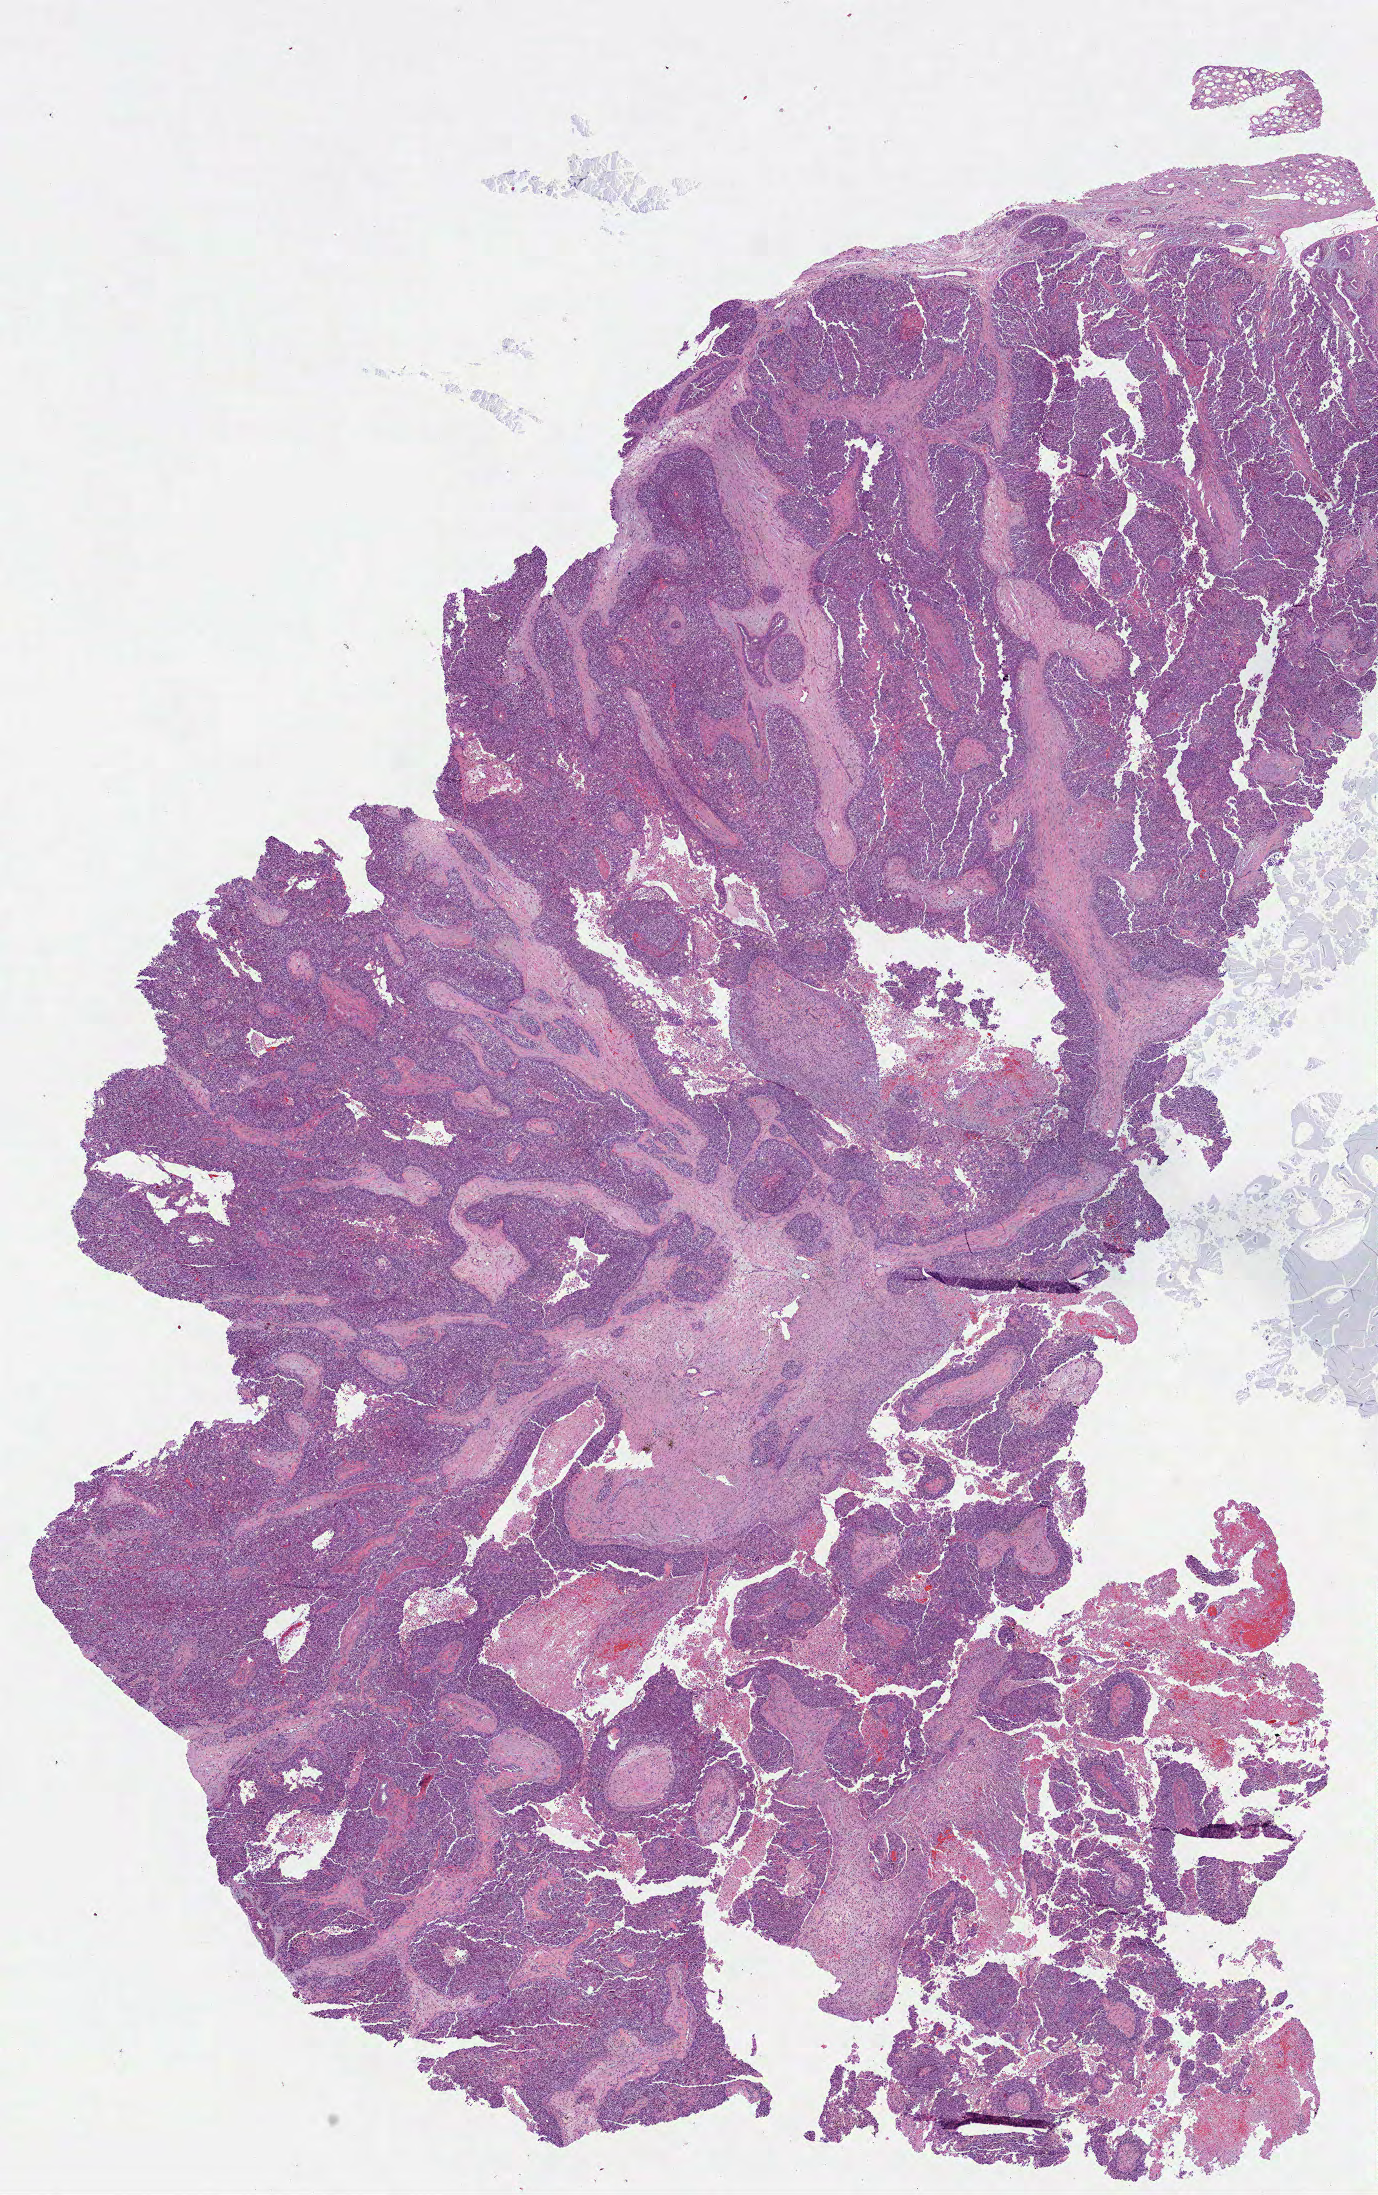
H&E-stained whole-slide image — shown as a low-resolution overview of the whole scanned area (about 11.1 x 17.7 mm); FFPE section; sample: primary tumour, breast. Female patient; age at initial diagnosis 72 years.
Histologic diagnosis: Infiltrating duct carcinoma, NOS.